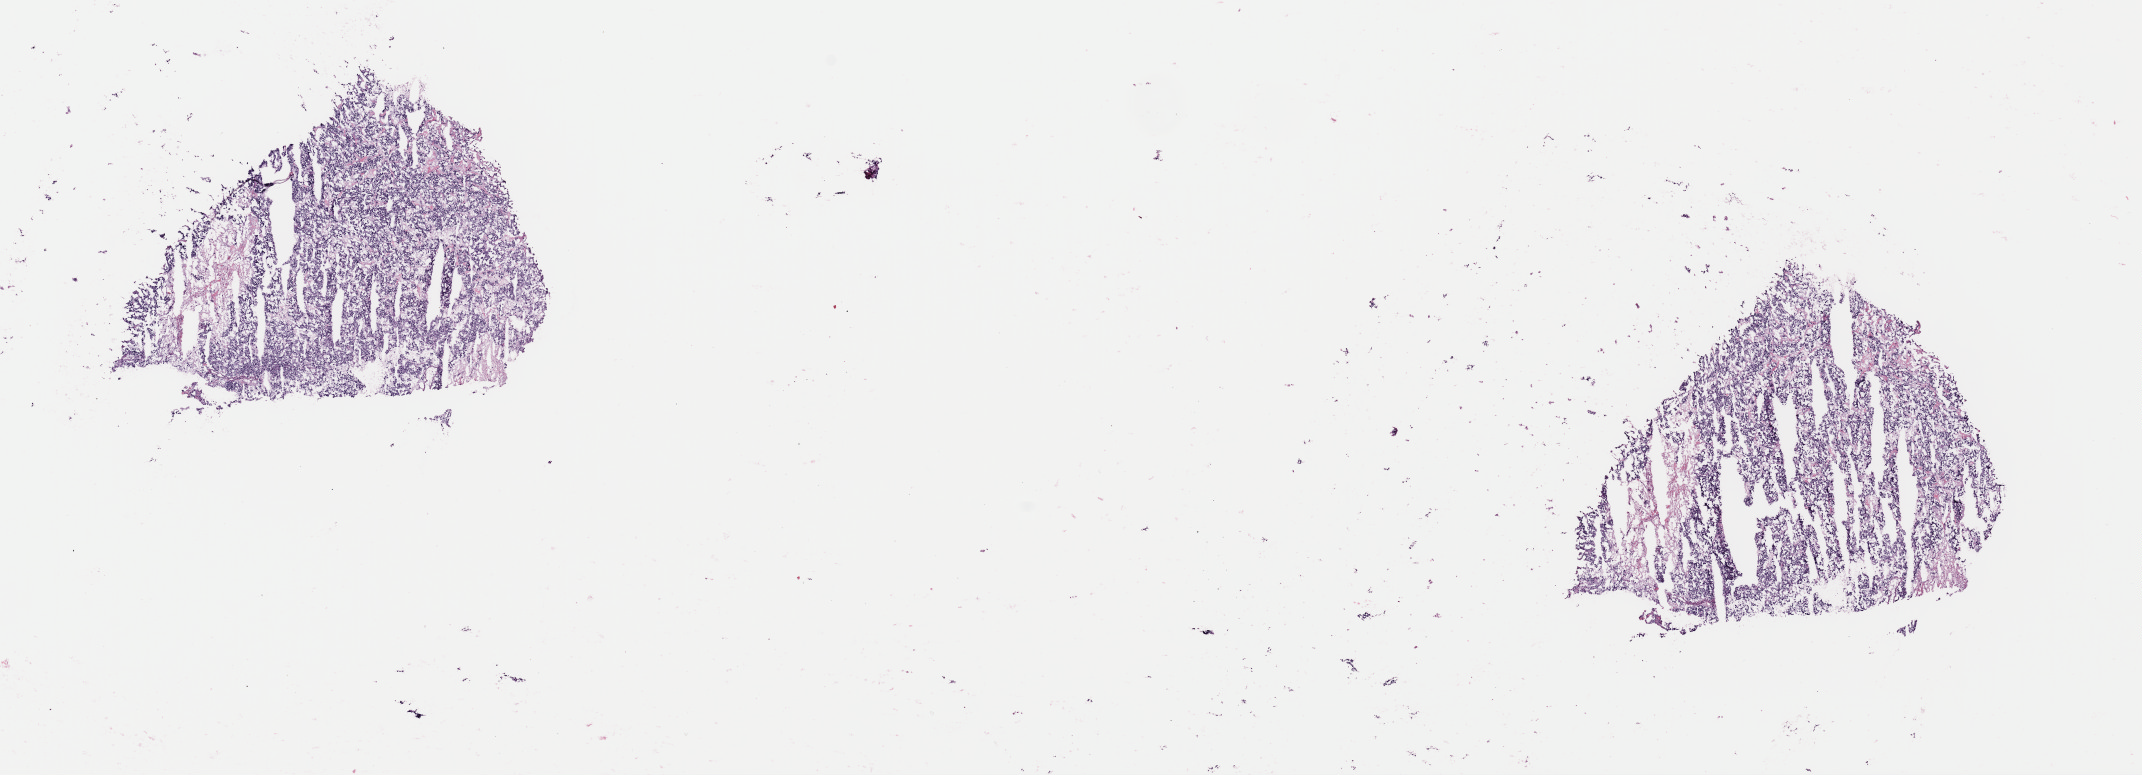
Hematoxylin and eosin (H&E) stained whole-slide image, whole scanned area (about 16.9 x 6.1 mm) shown as a low-resolution overview; frozen section from the top of the tissue portion; sample: primary tumour, retroperitoneum and peritoneum. Female, age 40 years at initial diagnosis. Composition of this section per pathologist review: tumour cells 90%, tumour nuclei 80%, normal cells 0%, stromal cells 0%, necrosis 10%. Infiltration values recorded for this section: lymphocyte infiltration 1%, monocyte infiltration 0%, neutrophil infiltration 0%.
Lymph nodes positive (case pathology): 0 of 1 examined. Diagnosis: Extra-adrenal paraganglioma, NOS (retroperitoneum).